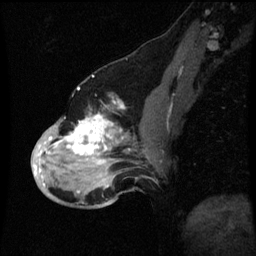
Breast MRI (dynamic contrast-enhanced), one sagittal slice. Dynamic contrast-enhanced series, image 2 of 3 at this slice position (ordered by acquisition). 1.5 T. TE 4.2 ms, TR 8.9 ms. 2 mm slice thickness. 256 × 256 image matrix, field of view 200 × 200 mm. Female patient, age 49 years. Case-level facts recorded for this patient, not image findings: setting: breast cancer imaged before/during neoadjuvant chemotherapy; receptor status: HR-positive, HER2-negative.
Structures marked on this image (semi-automatically segmented with operator editing):
- analysis volume of interest (the breast-tissue region the enhancement analysis was run in; not a lesion): bounding box [x1, y1, x2, y2] px = [32, 100, 153, 199]
- tumour enhancement mask (voxels above the 70 % enhancement threshold inside the analysis volume of interest): [34, 102, 125, 187]